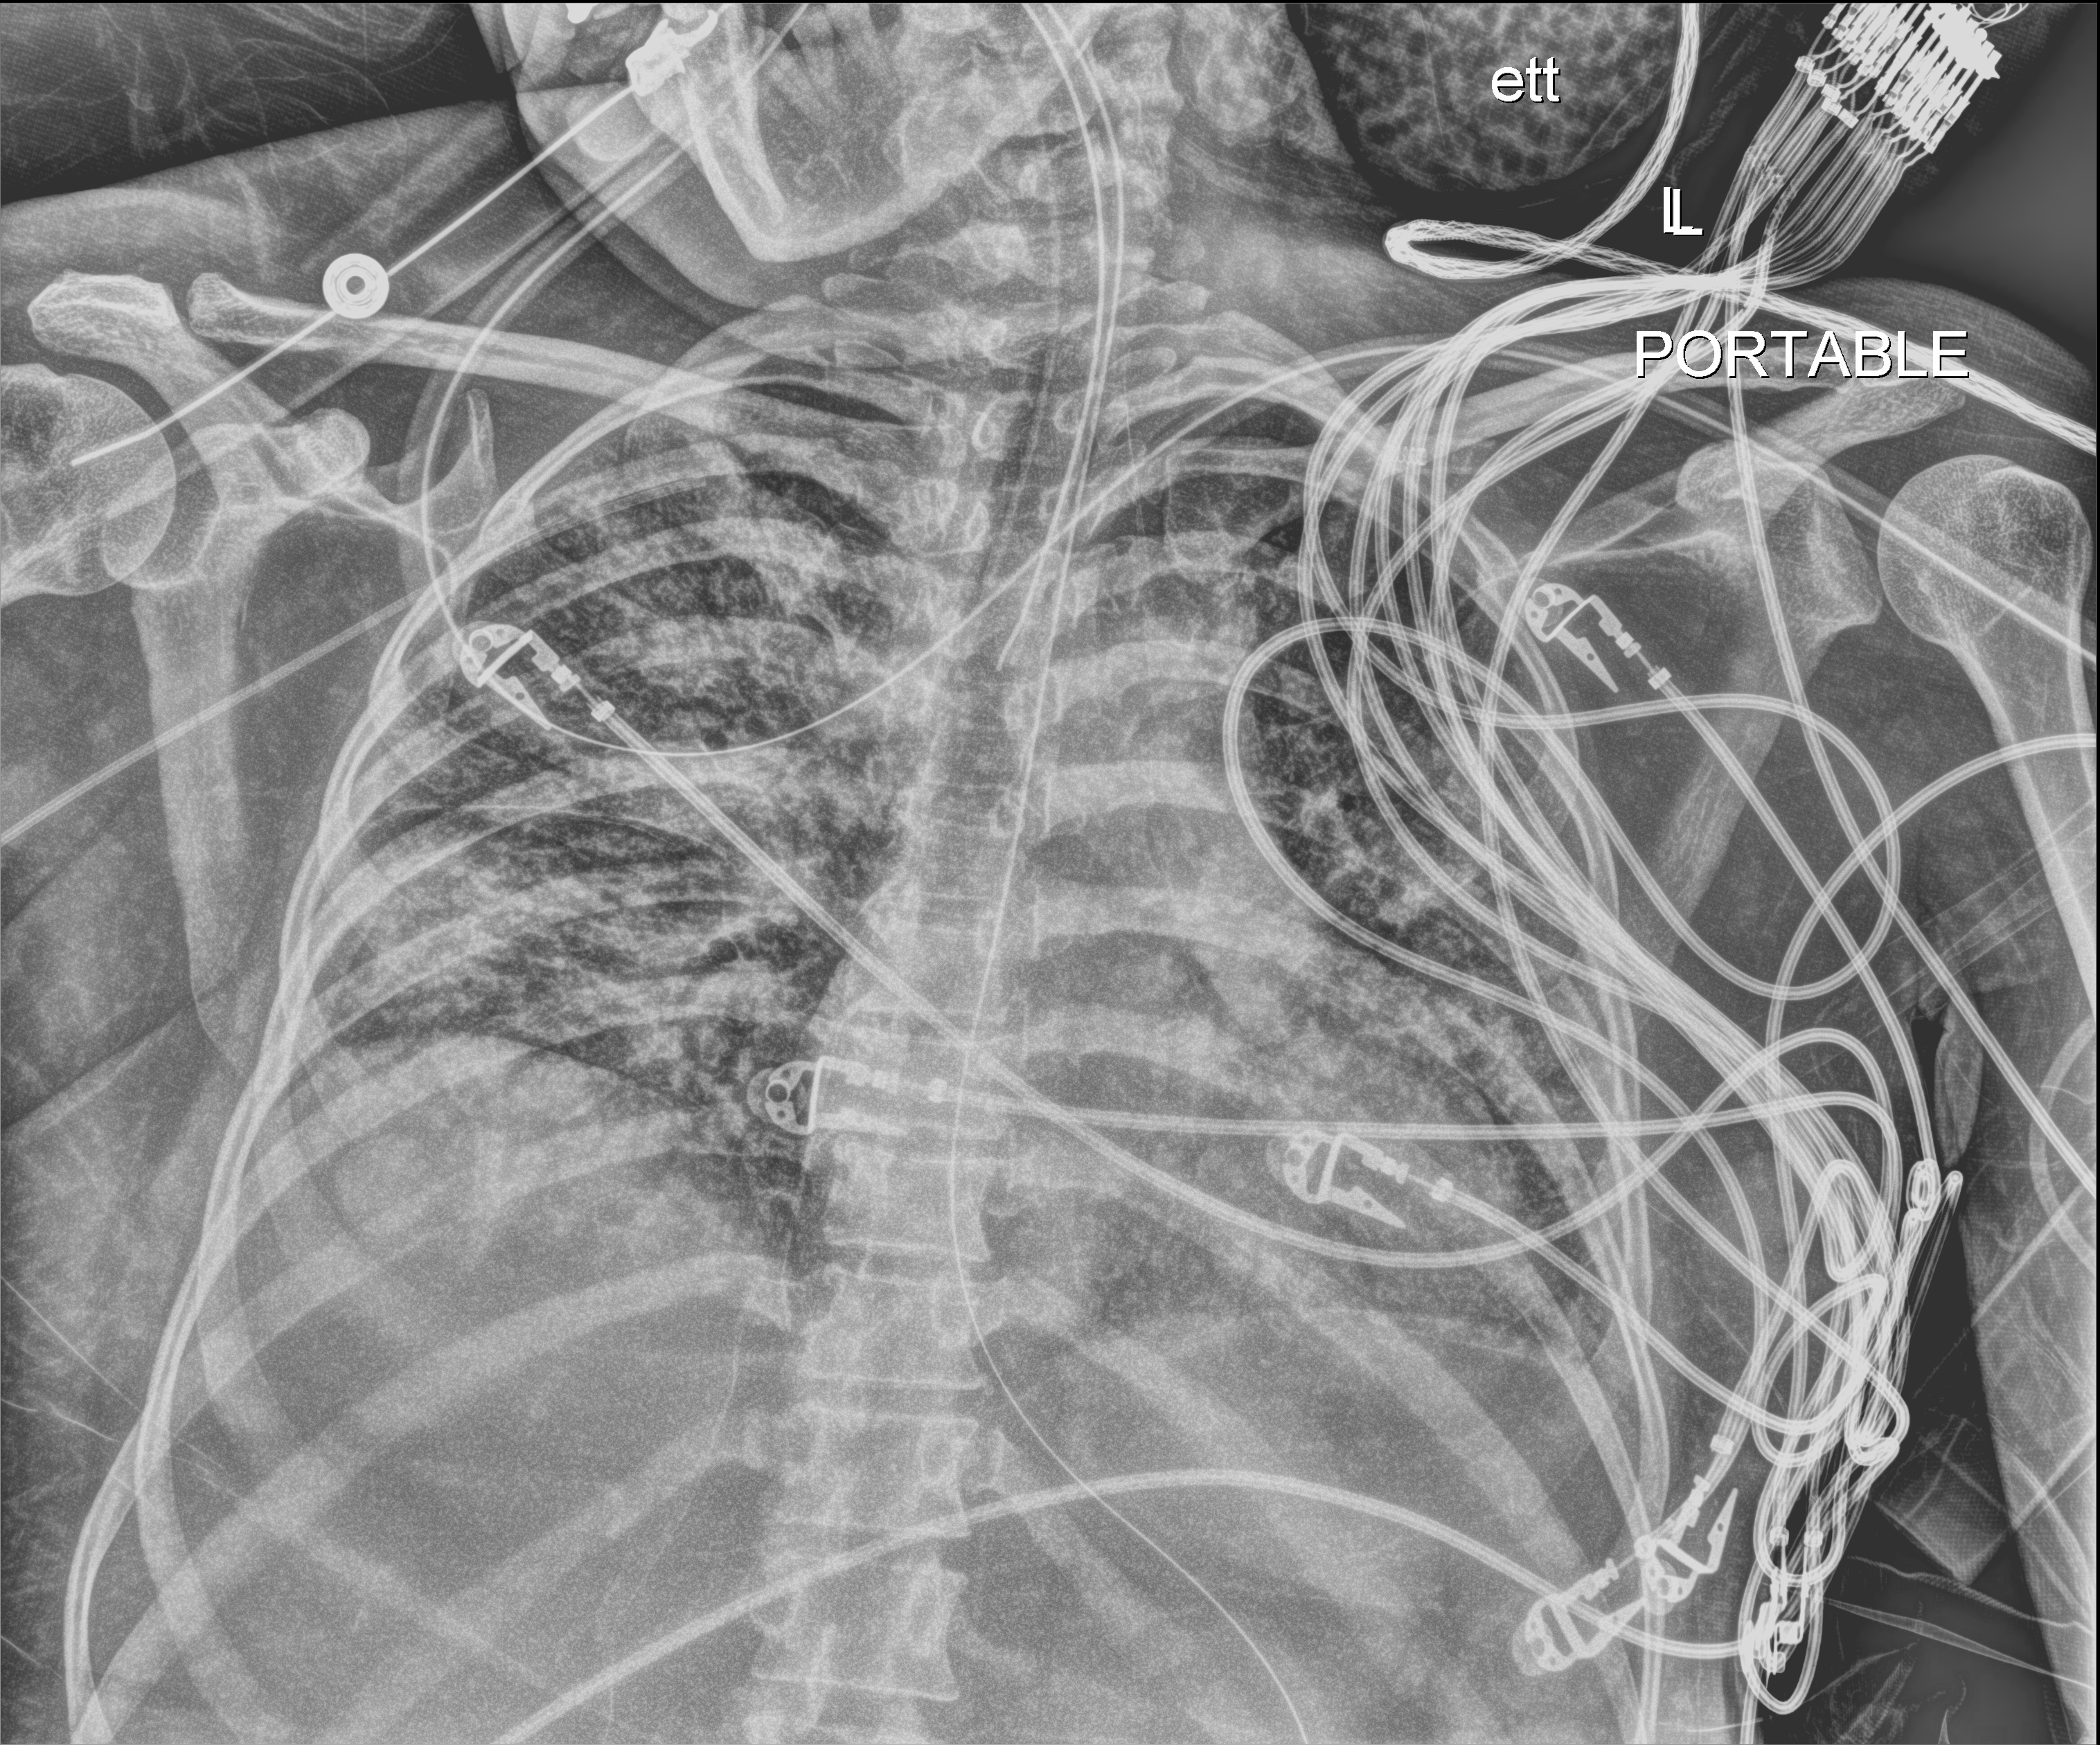
Bedside chest radiograph (digital radiography), anteroposterior (AP) projection. Patient hospitalised with COVID-19; female, aged 18–59 years.
Admission-level facts for this patient (not findings on this image; timing relative to this image not recorded): length of hospital stay: 71 days.